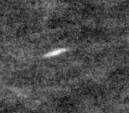
Region of interest cut from a scanned film mammogram (one marked finding); right breast; CC view.
Finding: calcifications, distribution regional; BI-RADS assessment category 2; subtlety rating 3 on a 1 (subtle) to 5 (obvious) scale; benign without callback (not worked up further).